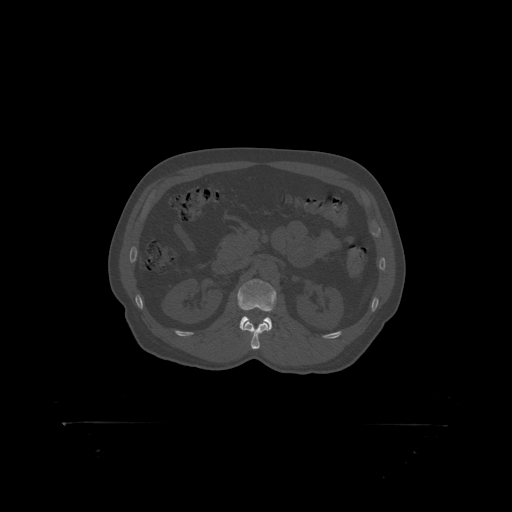
CT including the spine, one axial slice. Position 310 of 399 along the scan axis. Reconstruction kernel STANDARD. Bone window (W 1800 / L 400 HU). 1.25 mm slice thickness. 512 × 512 image matrix, field of view 650 × 650 mm. Male patient, age 46 years. From the clinical record (not read from this slice): primary cancer: skin.
Annotated regions visible in this slice (semi-automatic segmentation, software-assisted and operator-edited):
- L2 vertebra: bounding box (x1, y1, x2, y2) in pixels: (238, 279, 277, 319)